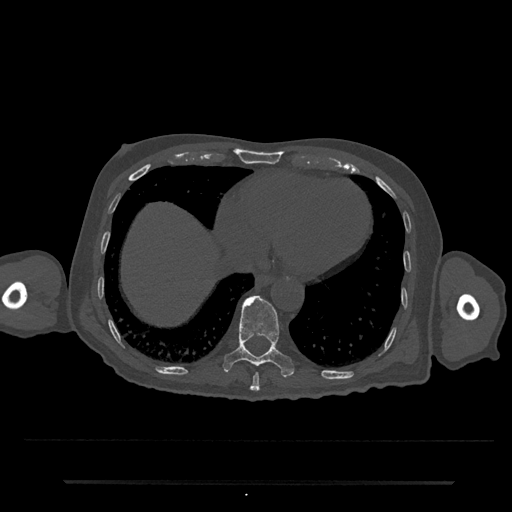
CT including the spine, one axial slice. Position 318 of 797 along the scan axis. Reconstruction kernel Br40s/3. Bone window (W 1800 / L 400 HU). 0.5 mm slice thickness. 512 × 512 image matrix, field of view 427 × 427 mm. Male patient, age 74 years. Case-level facts recorded for this patient, not image findings: primary cancer: prostate.
Outlined on this slice (semi-automatic segmentation, software-assisted and operator-edited):
- T10 vertebra: box from (x=222, y=295) to (x=294, y=378) px
- T9 vertebra: (x=250, y=373)–(x=260, y=392)